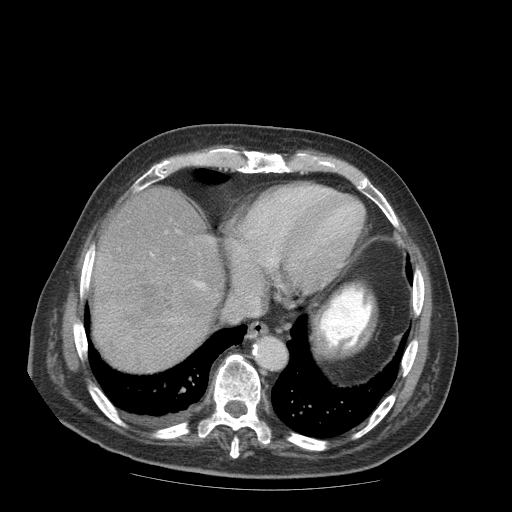
Contrast-enhanced abdominal CT (liver protocol), one axial slice; position 78 of 99 along the scan axis; reconstruction kernel STANDARD; 140 kVp; soft-tissue window (W 400 / L 40 HU); 512 × 512 image matrix. Case-level facts recorded for this patient, not image findings: diagnosis: hepatocellular carcinoma (patient treated with transarterial chemoembolisation; whether this scan precedes or follows treatment is not stated here); TNM stage (as recorded): Stage-IIIB; Child-Pugh class: A; tumour nodularity: multinodular.
Annotated regions visible in this slice (semi-automatic segmentation, software-assisted and operator-edited):
- liver parenchyma outside the tumour (the mass and vessels are separate outlines, so this box may not span the whole liver): bounding box (x1, y1, x2, y2) in pixels: (92, 188, 224, 372)
- mass: (93, 248, 178, 347)
- liver vessels: (151, 253, 205, 320)